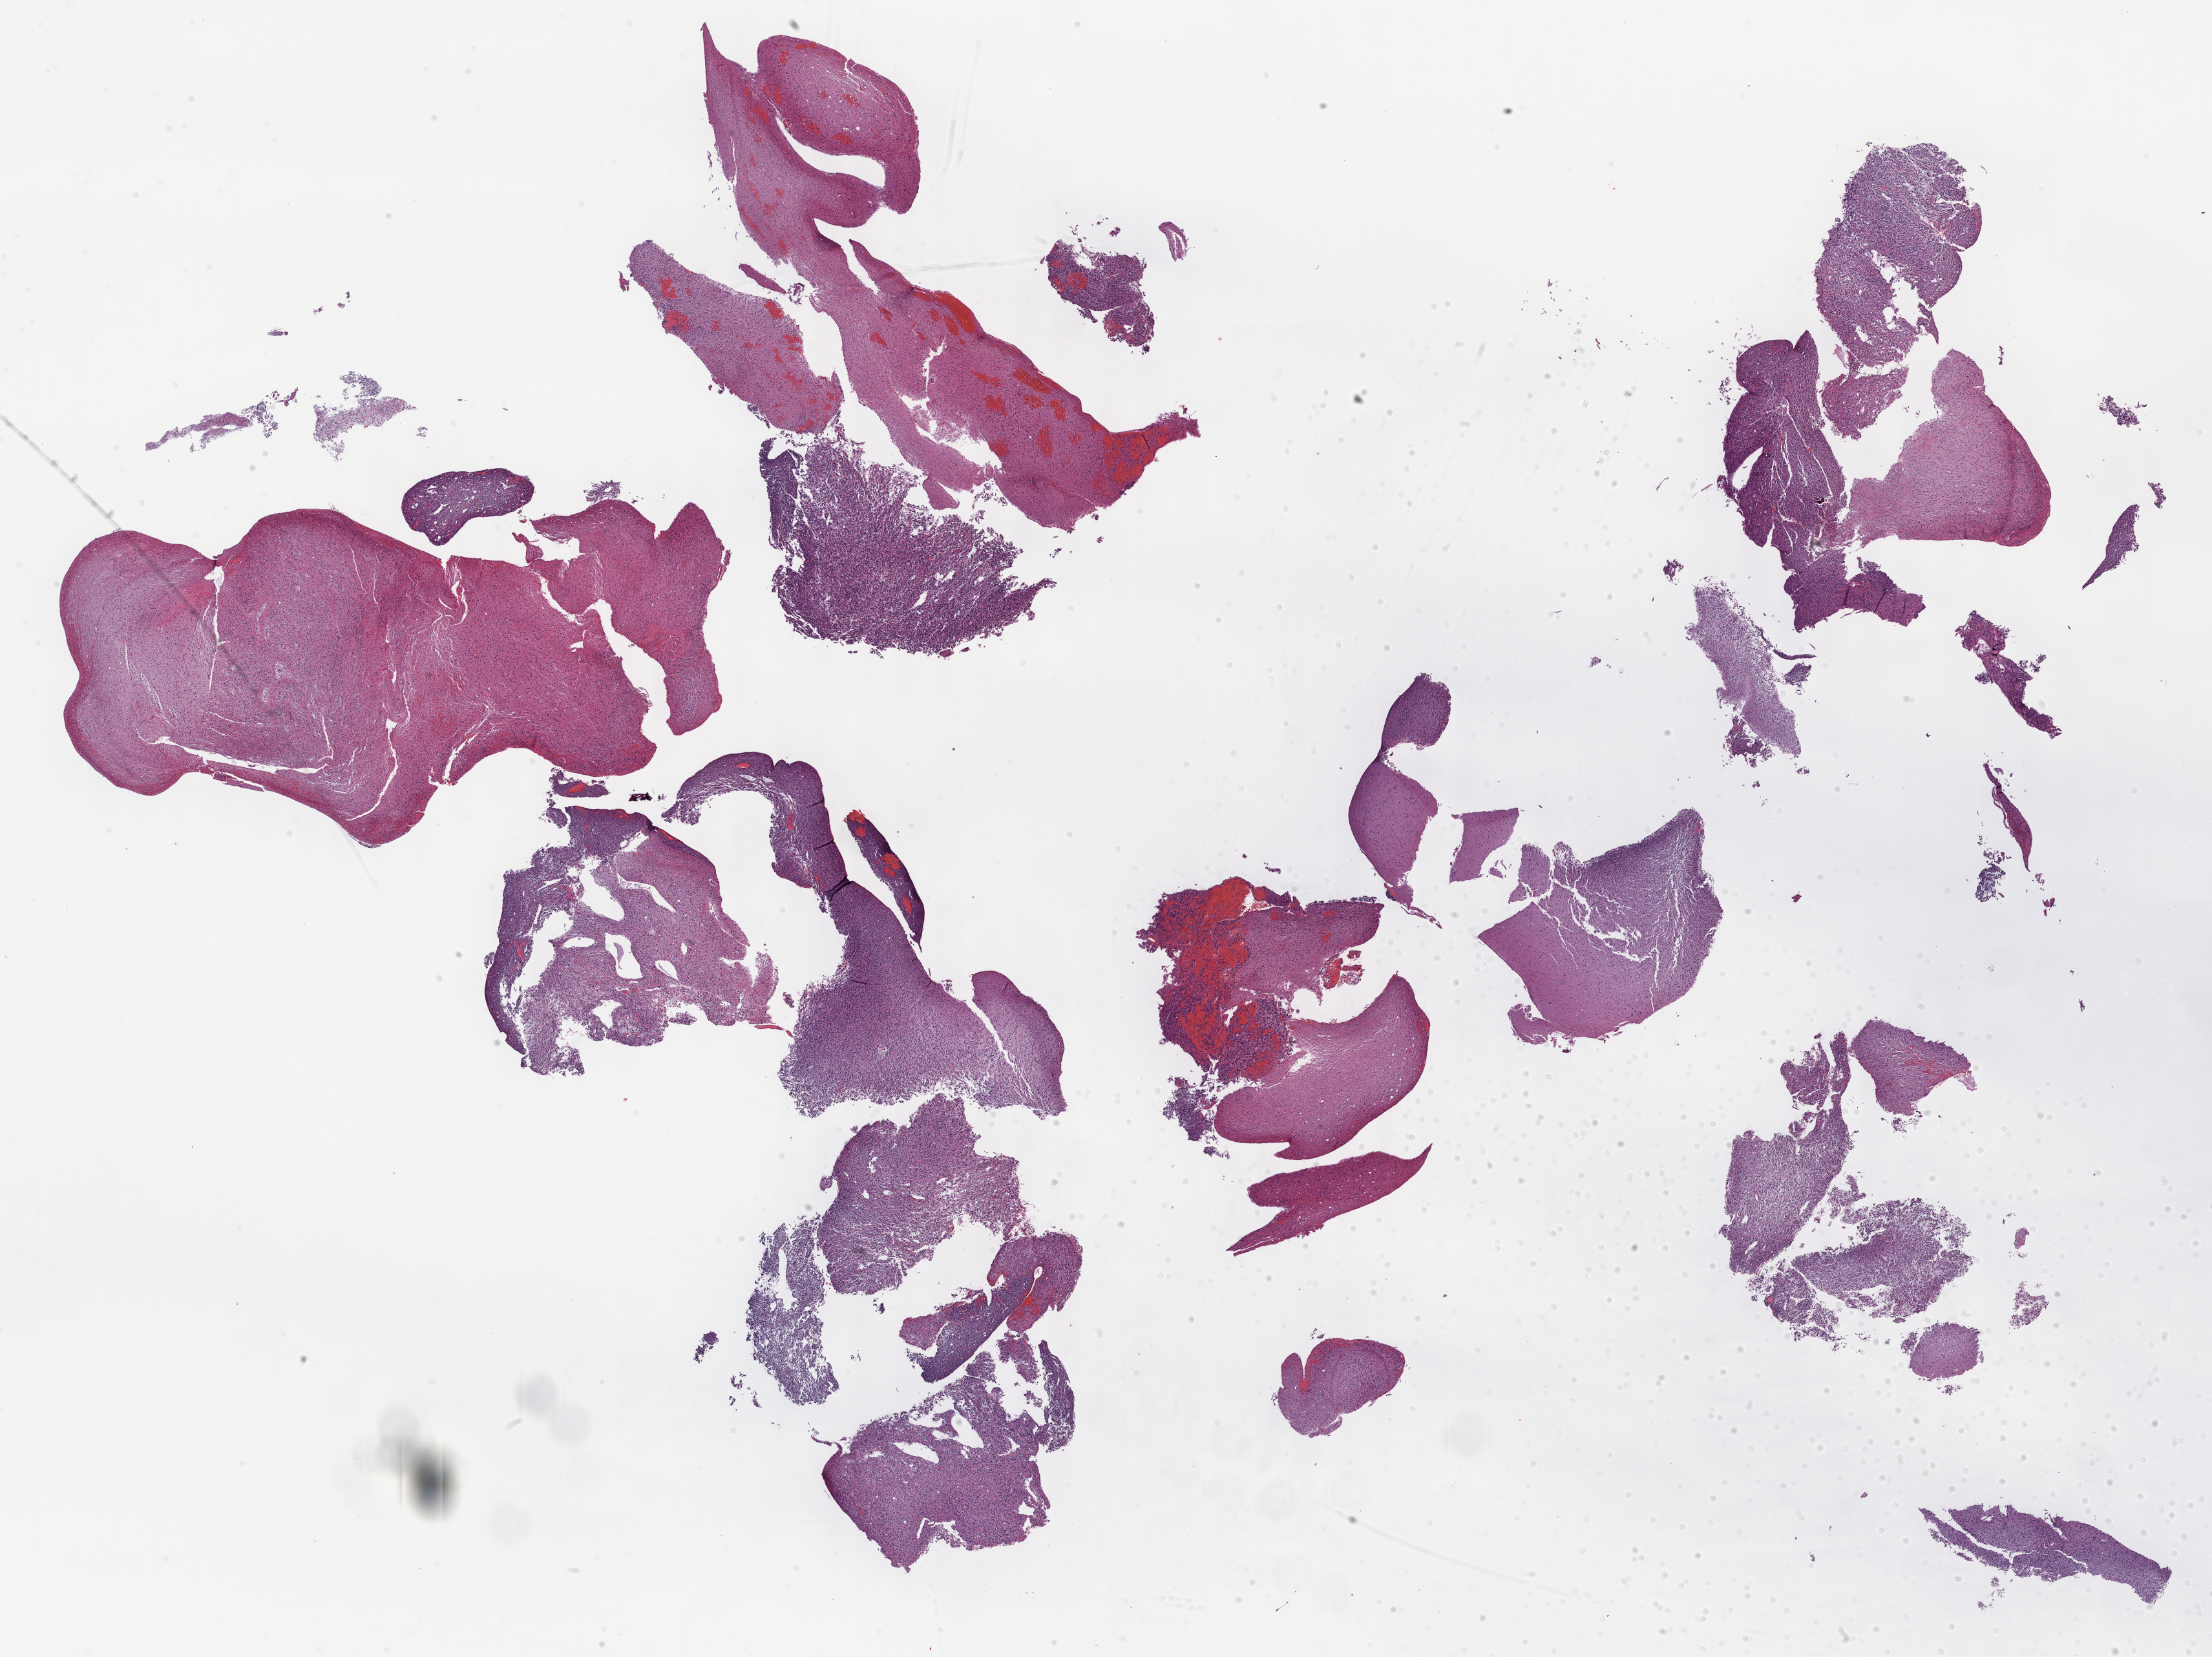
H&E-stained whole-slide image, a low-resolution overview of the entire scanned area, about 27.7 x 20.7 mm. Formalin-fixed paraffin-embedded (FFPE) diagnostic section. Sample: primary tumour, brain. Female, age 44 years at initial diagnosis. Histologic grade: G3 (poorly differentiated).
Laterality: left. Diagnosis: Astrocytoma, anaplastic.